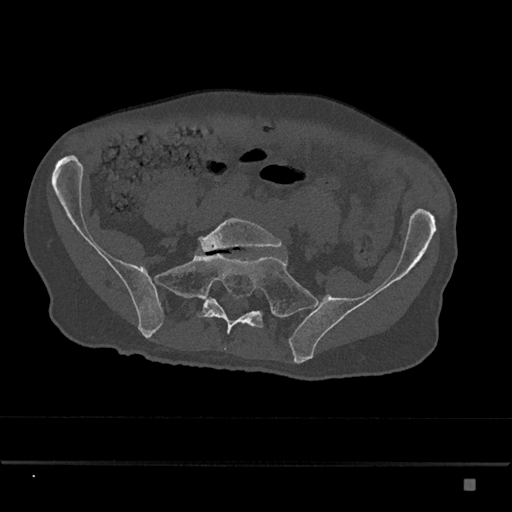
CT including the spine, one axial slice. Position 229 of 797 along the scan axis. Bone window (W 1800 / L 400 HU). 0.5 mm slice thickness. 512 × 512 image matrix, field of view 390 × 390 mm. Male patient, age 72 years. Case-level facts recorded for this patient, not image findings: primary cancer: prostate.
Structures marked on this image (semi-automatic segmentation, software-assisted and operator-edited):
- L5 vertebra: box from (x=199, y=218) to (x=283, y=252) px